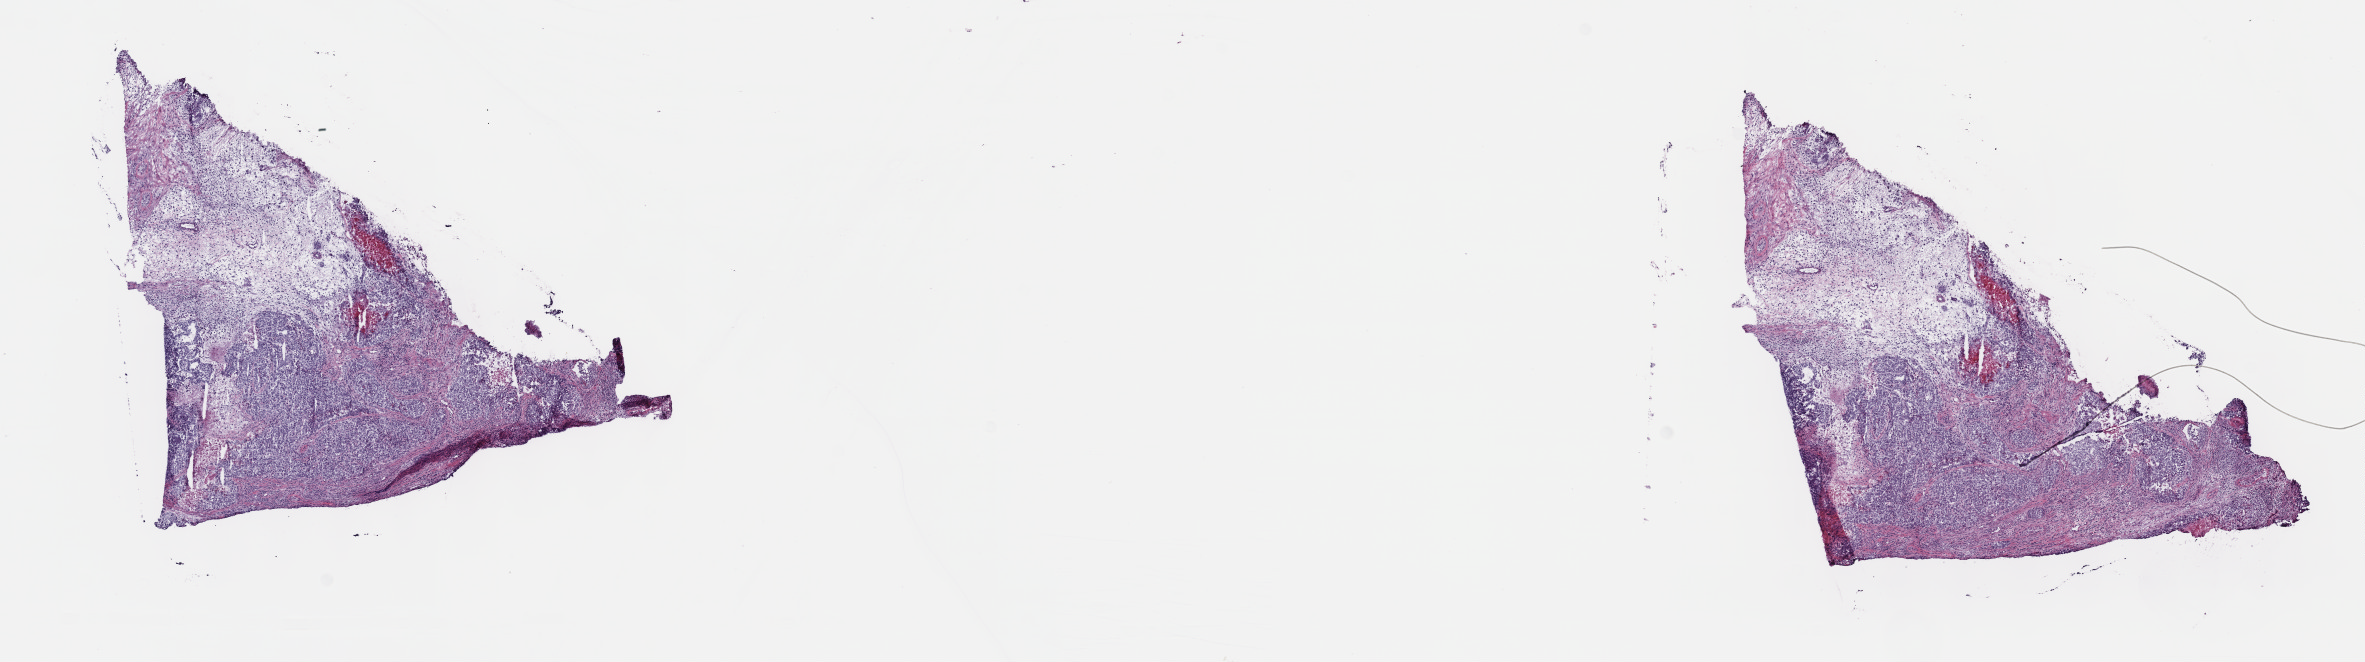
H&E-stained whole-slide image, shown as a low-resolution overview of the whole scanned area (about 19.1 x 5.4 mm, acquisition: 40x scan); frozen section from the top of the tissue portion; testis, primary tumour sample. Male patient; age at initial diagnosis 23 years. Composition of this section per pathologist review: tumour cells 90%, tumour nuclei 95%, normal cells 0%, stromal cells 0%, necrosis 10%. Infiltration values recorded for this section: lymphocyte infiltration 0%, monocyte infiltration 0%, neutrophil infiltration 0%.
AJCC pathologic stage: IS (7th edition). Histologic diagnosis: Mixed germ cell tumor. Laterality: bilateral.